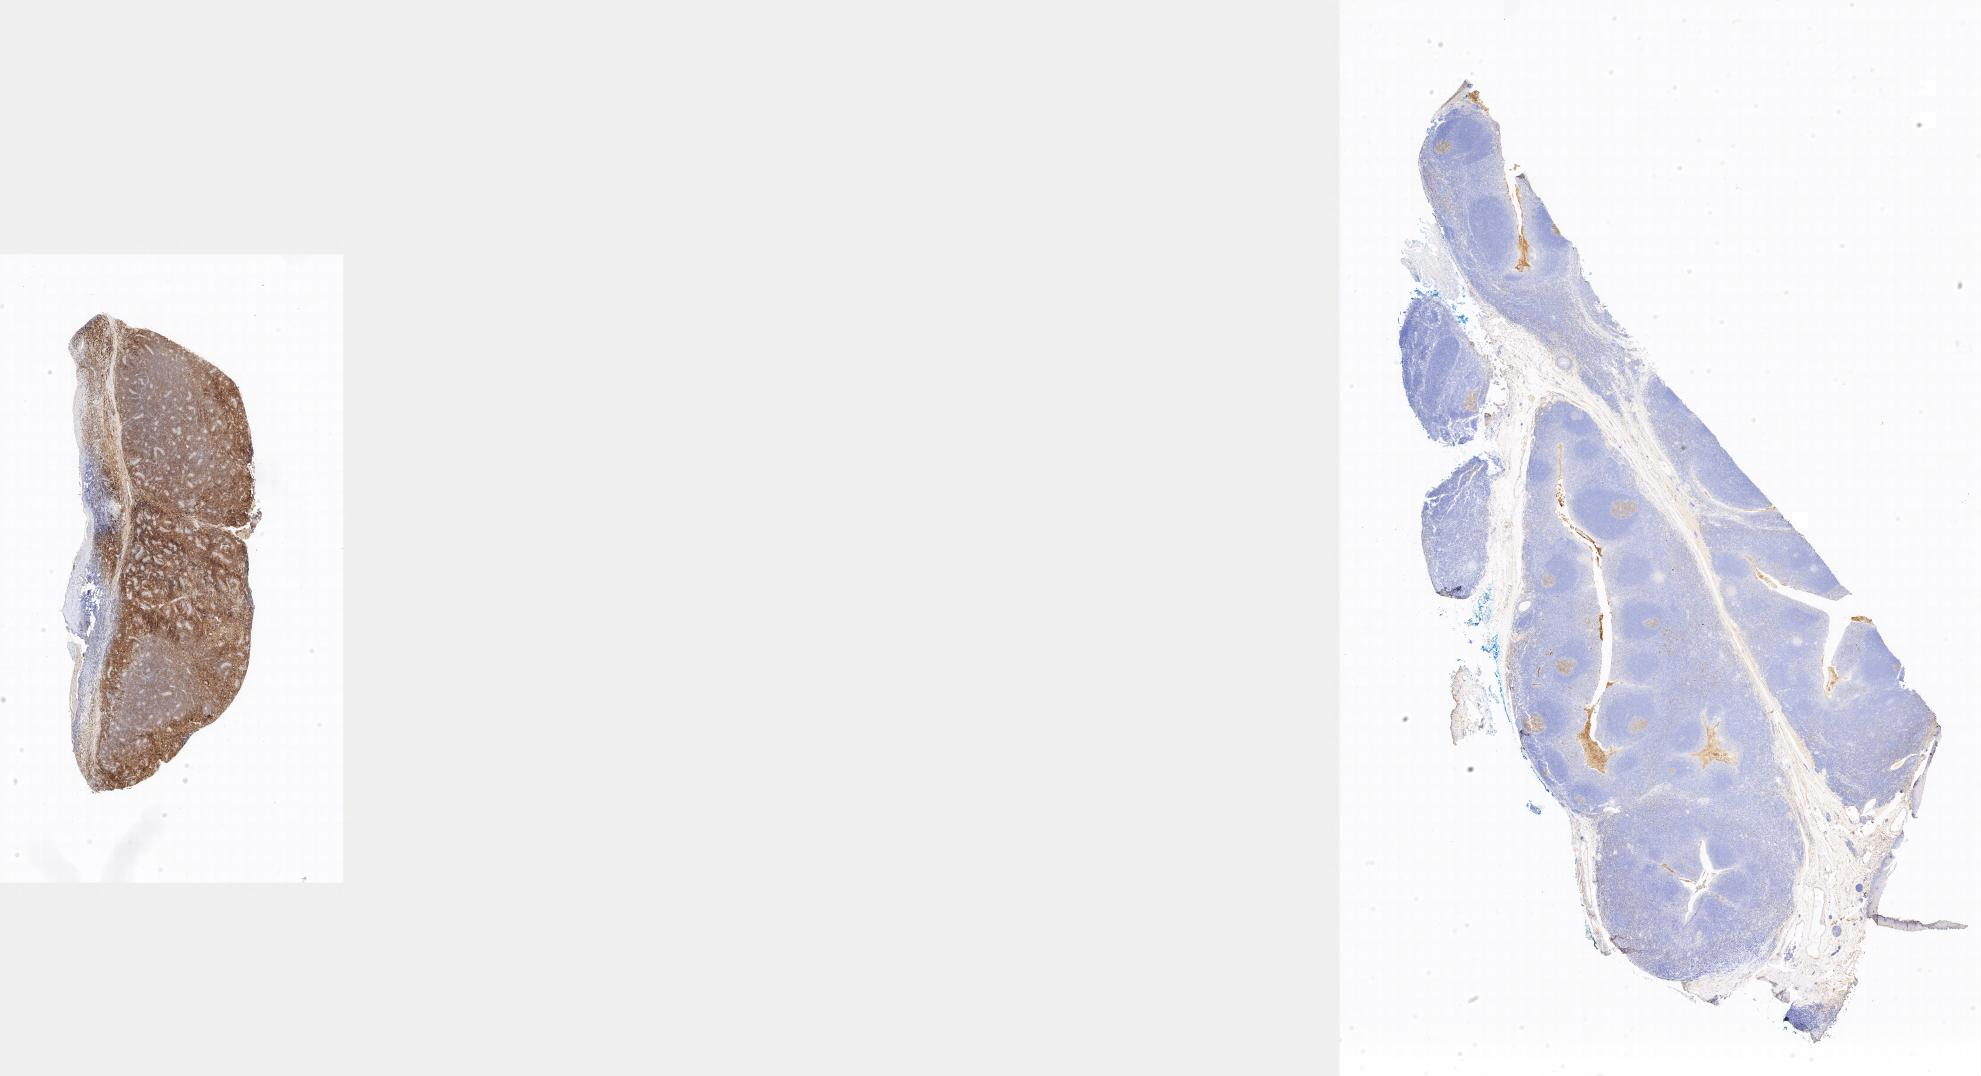
Whole-slide image, immunohistochemical stain for CD10 — whole scanned area shown as a low-resolution overview. Specimen: tumor tissue. Anatomic site: testis. Male patient; age at initial diagnosis 8 years.
Histologic diagnosis: Burkitt lymphoma, NOS.